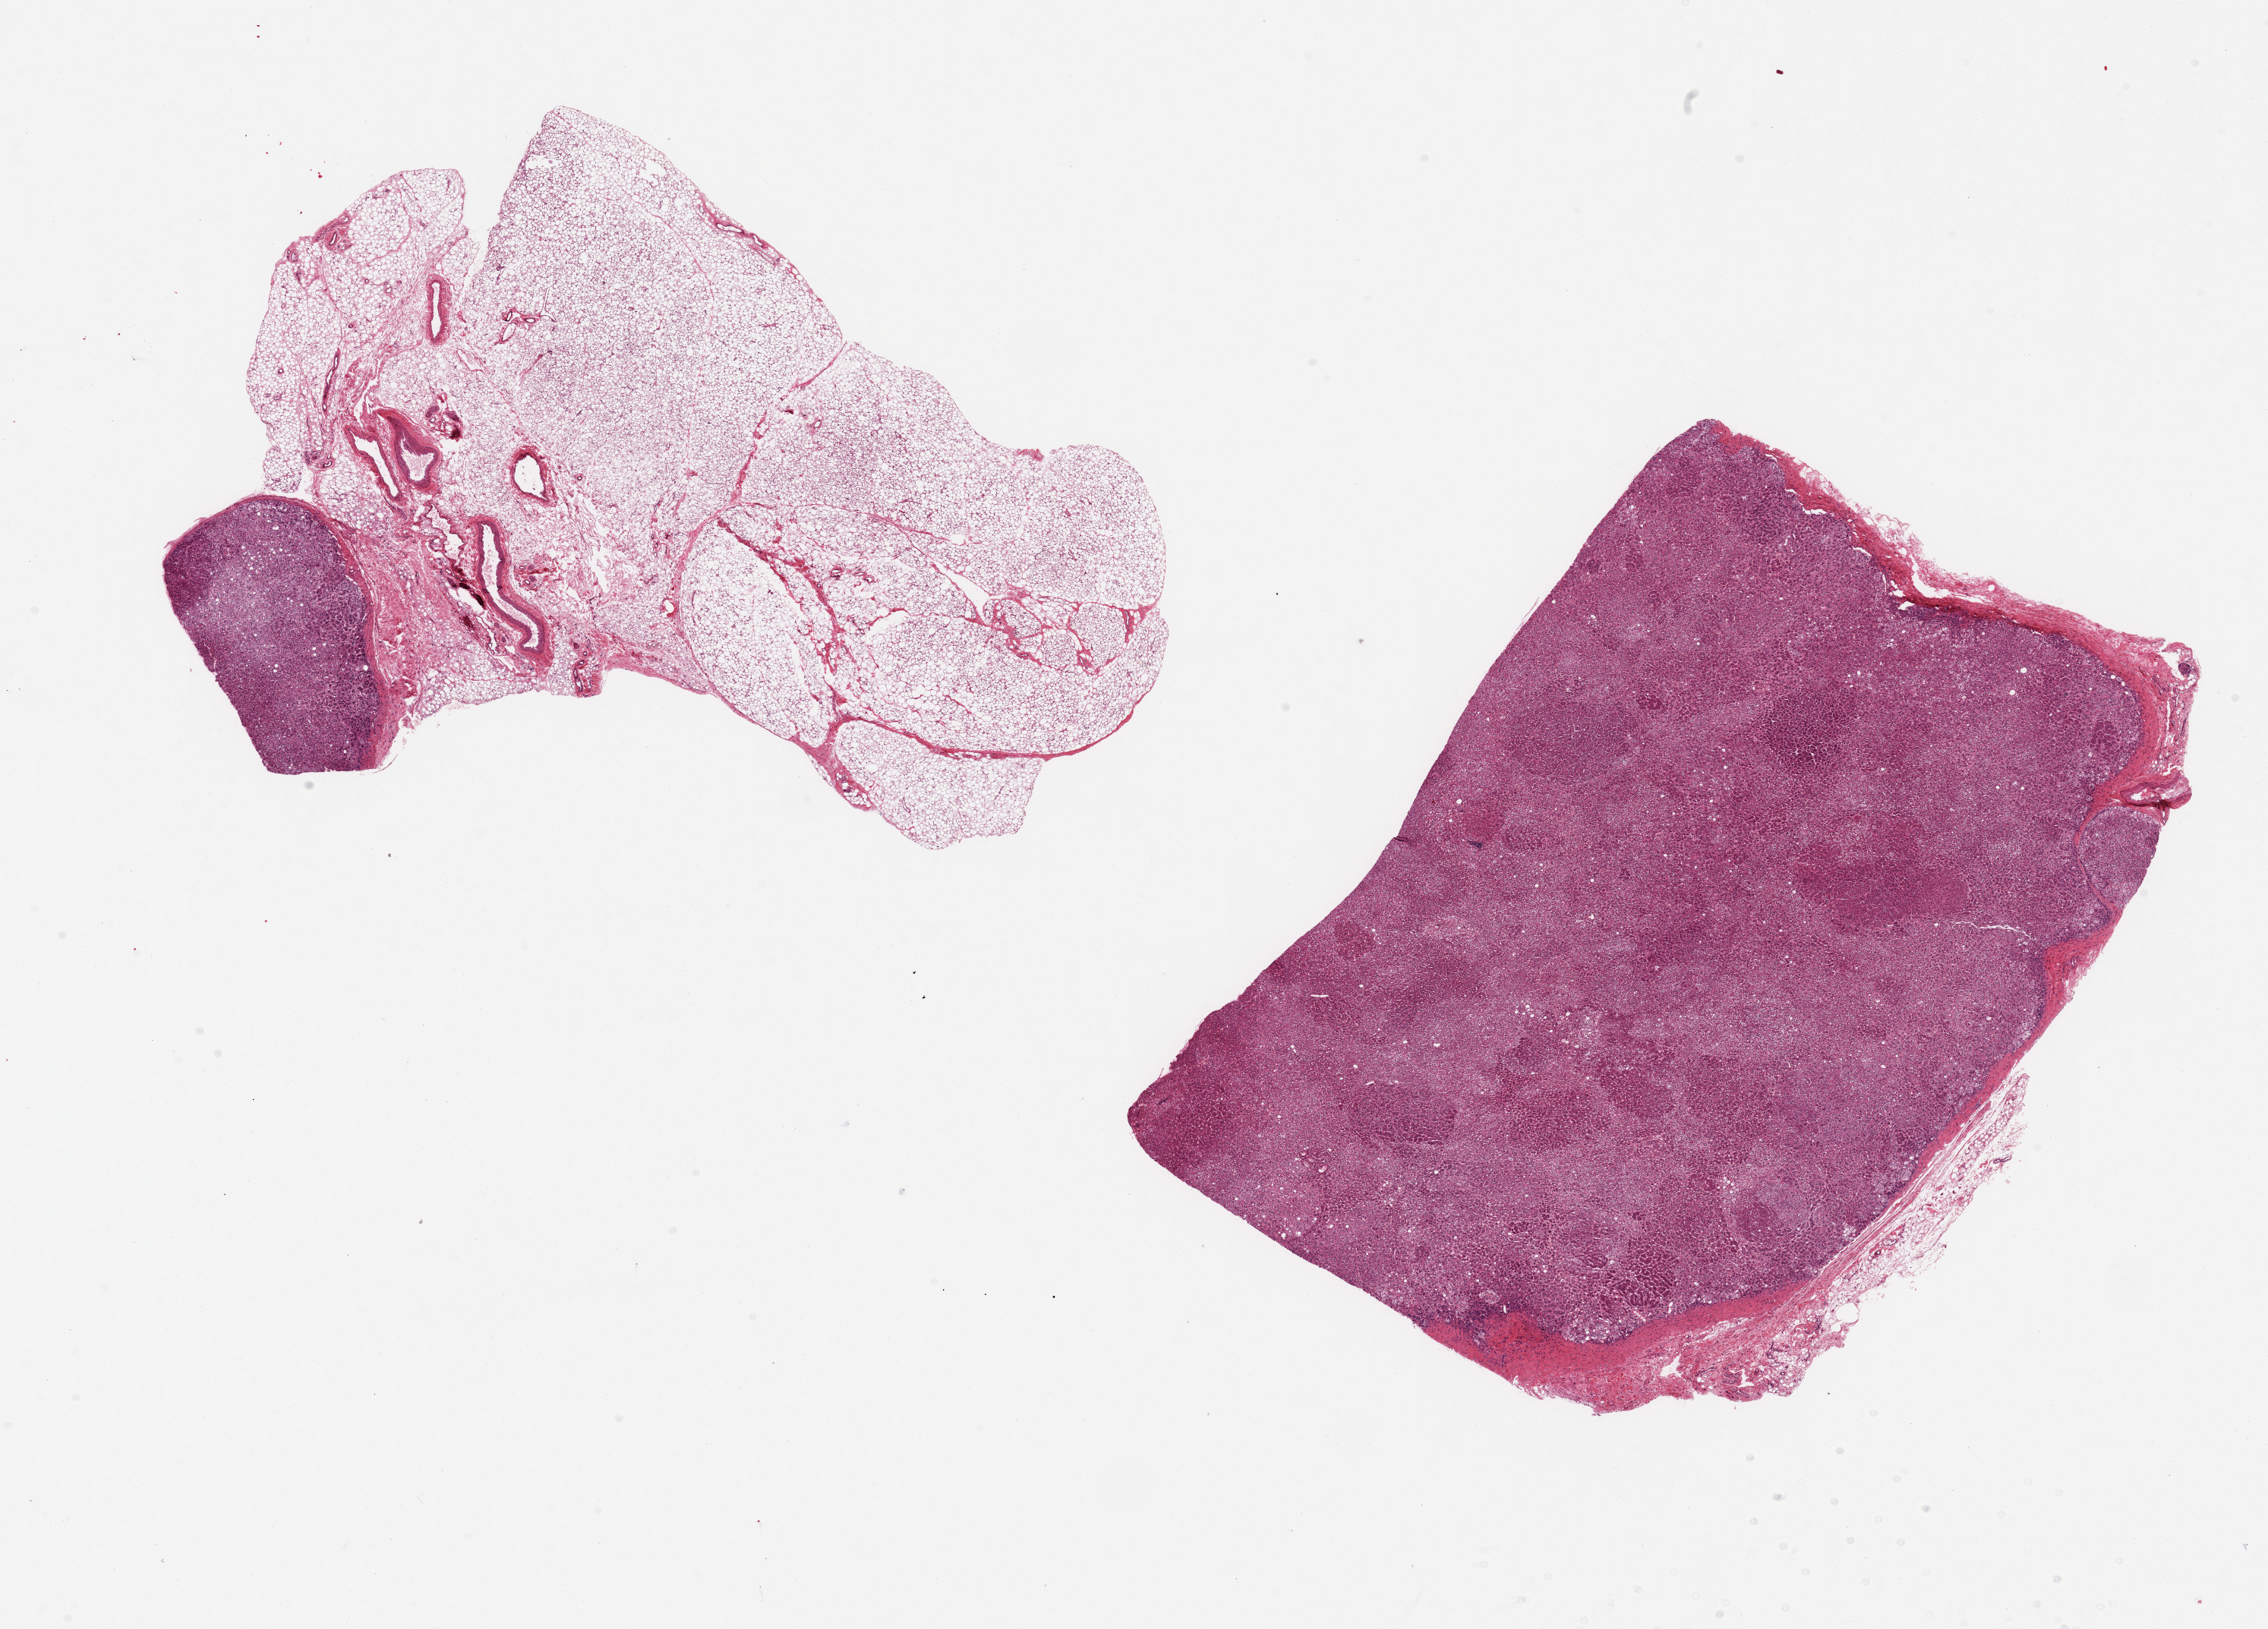
Digitized H&E-stained section, brightfield — whole scanned area (about 23.6 x 17.0 mm, slide scanned at 20x) shown as a low-resolution overview.
- specimen: PAXgene-fixed, paraffin-embedded tissue; target tissue: adrenal gland; donor tissue sample